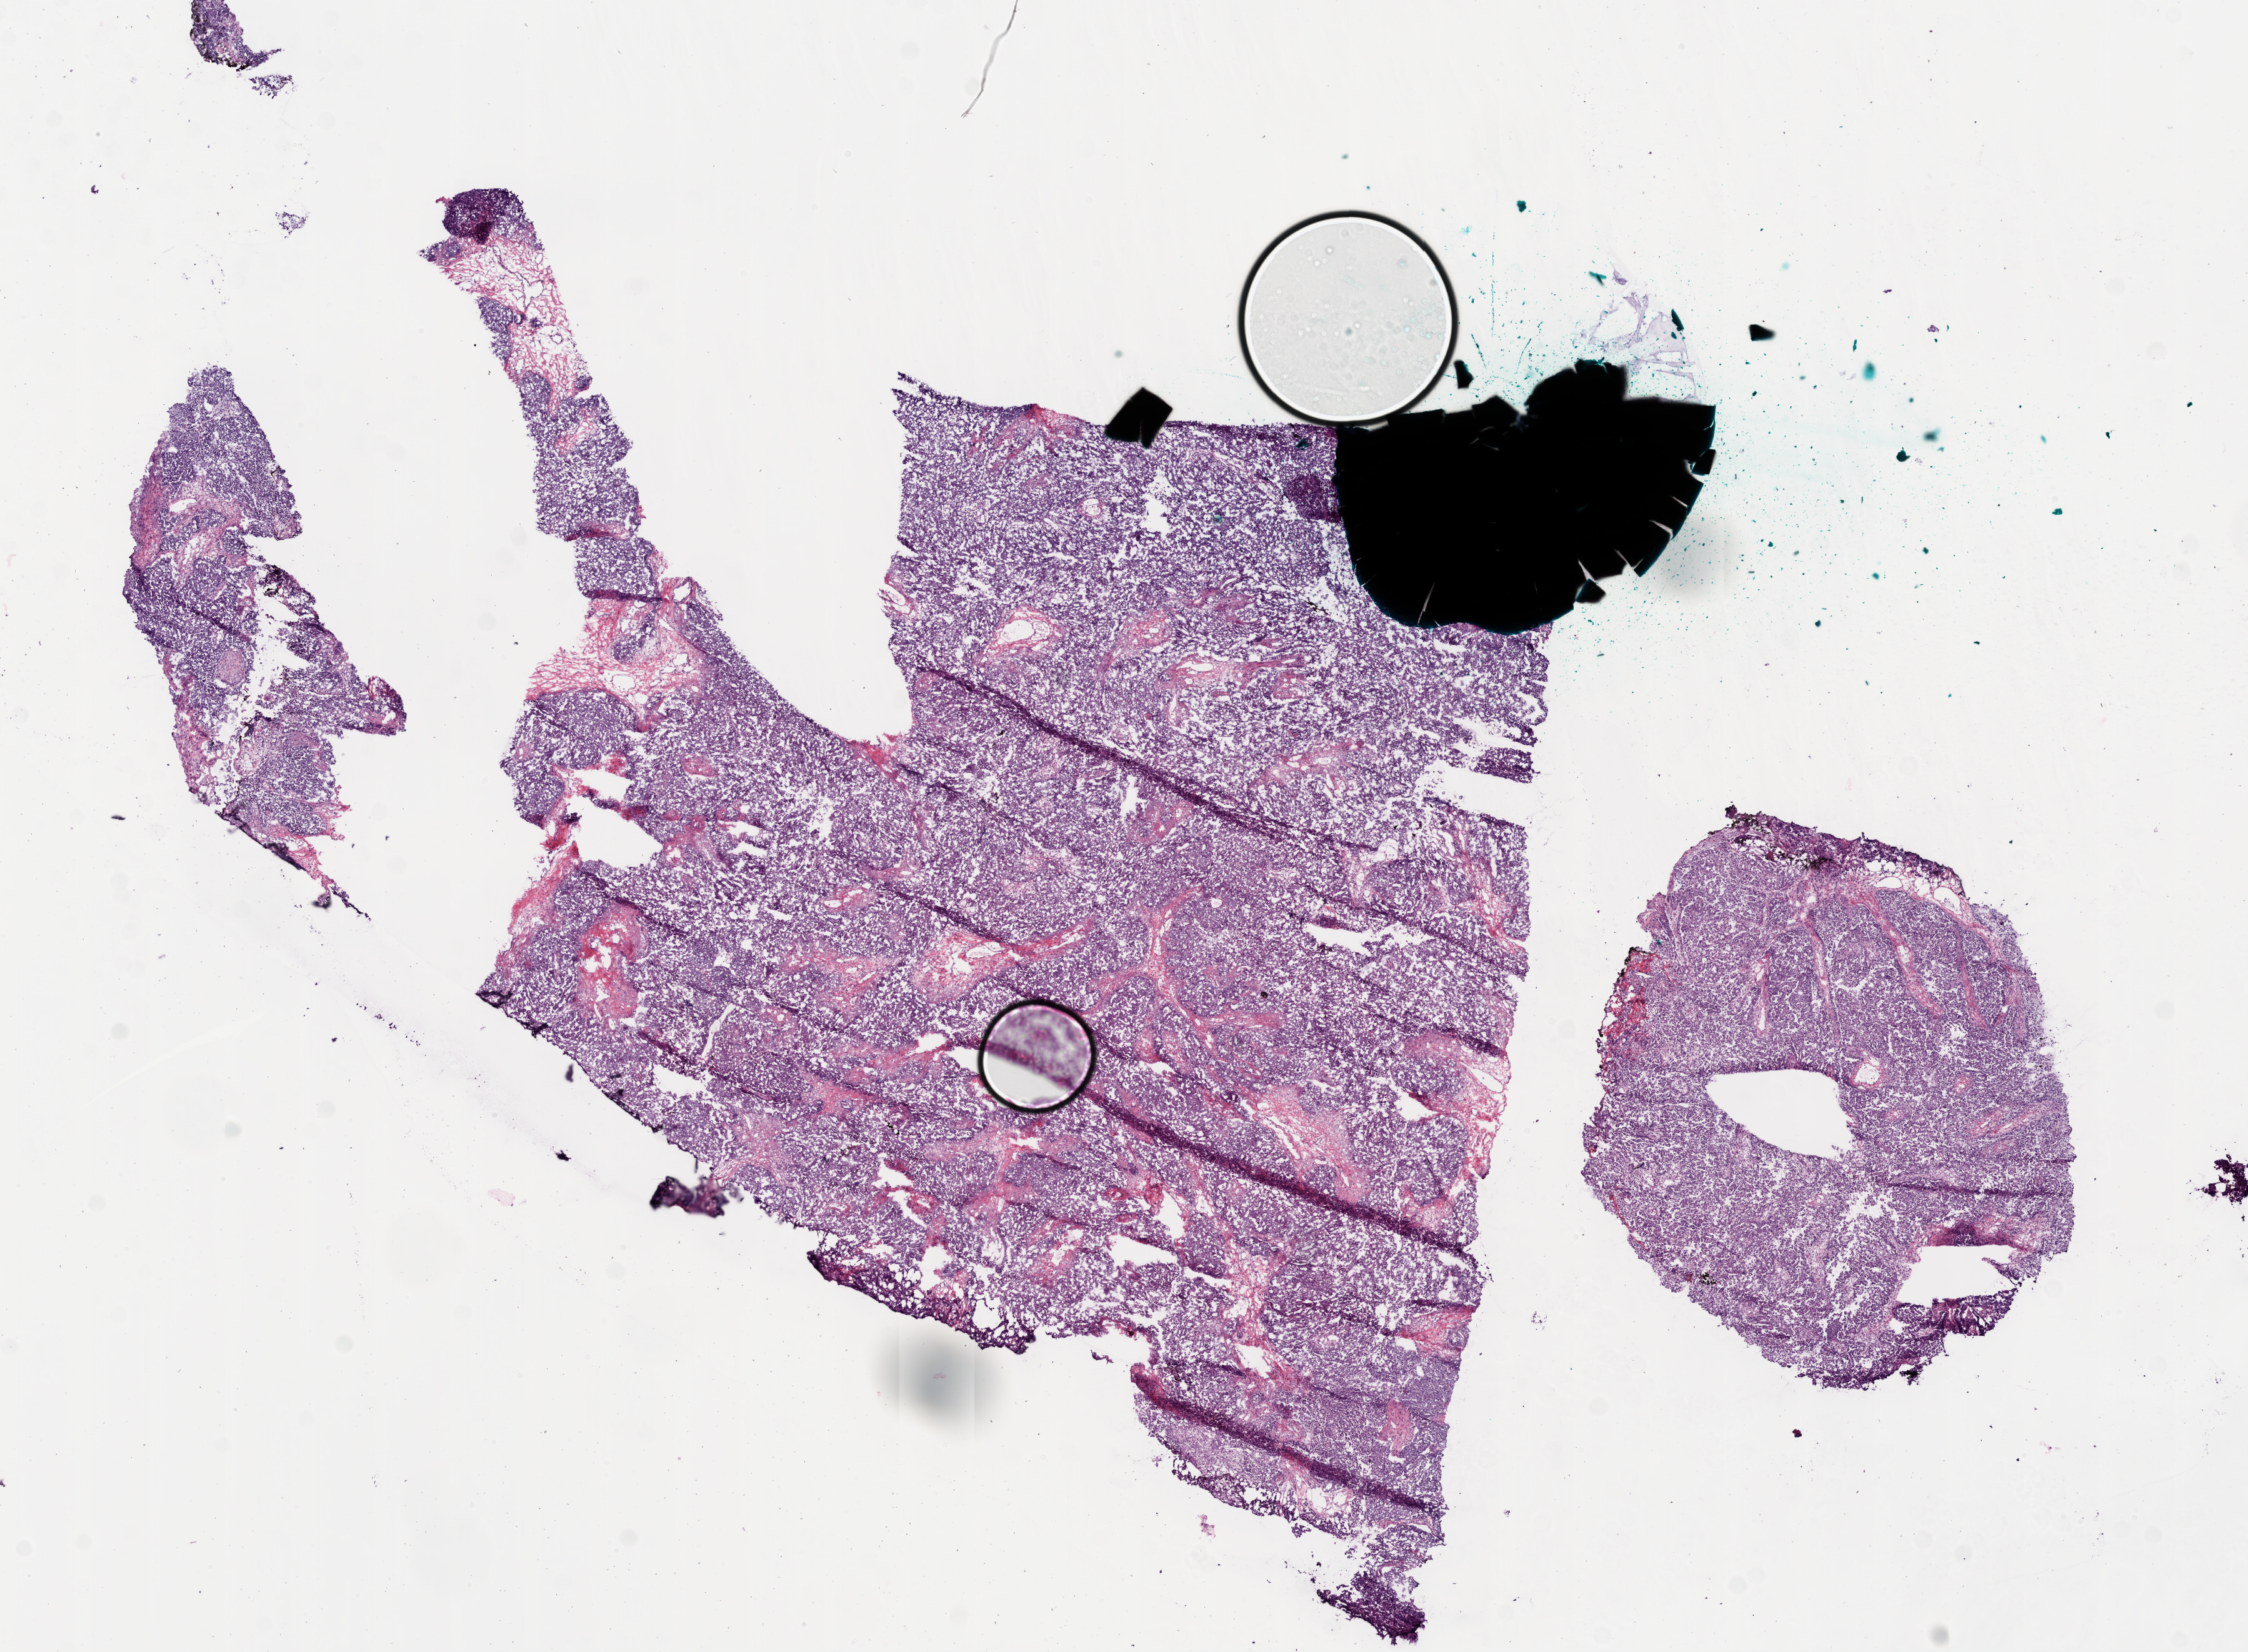
Whole-slide histology image, H&E-stained — low-resolution overview of the scanned area, about 14.5 x 10.7 mm (slide scanned at 20x). Frozen section from the bottom of the tissue portion. Ovary, primary tumour sample. Patient: female, age at initial diagnosis 59 years.
Histologic diagnosis: Serous cystadenocarcinoma, NOS.